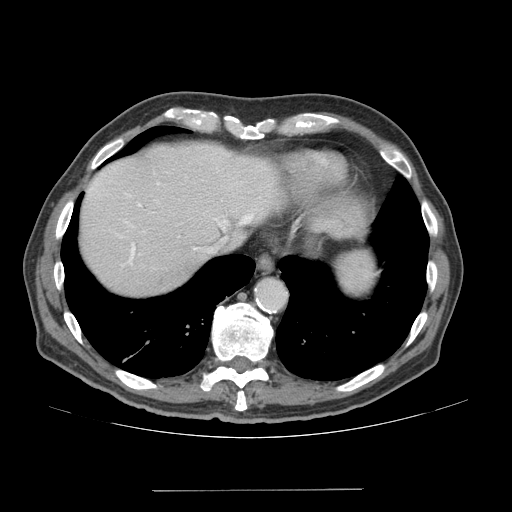
Contrast-enhanced abdominal CT (liver protocol), one axial slice; position 60 of 77 along the scan axis; reconstruction kernel STANDARD; 140 kVp; soft-tissue window (W 400 / L 40 HU); 512 × 512 image matrix, field of view 400 × 400 mm. Case-level facts recorded for this patient, not image findings: diagnosis: hepatocellular carcinoma (patient treated with transarterial chemoembolisation; whether this scan precedes or follows treatment is not stated here); TNM stage (as recorded): Stage-IVA; Child-Pugh class: A; tumour differentiation: well differentiated; tumour nodularity: uninodular.
Outlined on this slice (semi-automatically segmented with operator editing):
- abdominal aorta: bounding box (x1, y1, x2, y2) in pixels: (257, 281, 286, 309)
- liver parenchyma outside the tumour (the mass and vessels are separate outlines, so this box may not span the whole liver): (80, 142, 284, 296)
- liver vessels: (89, 182, 257, 266)